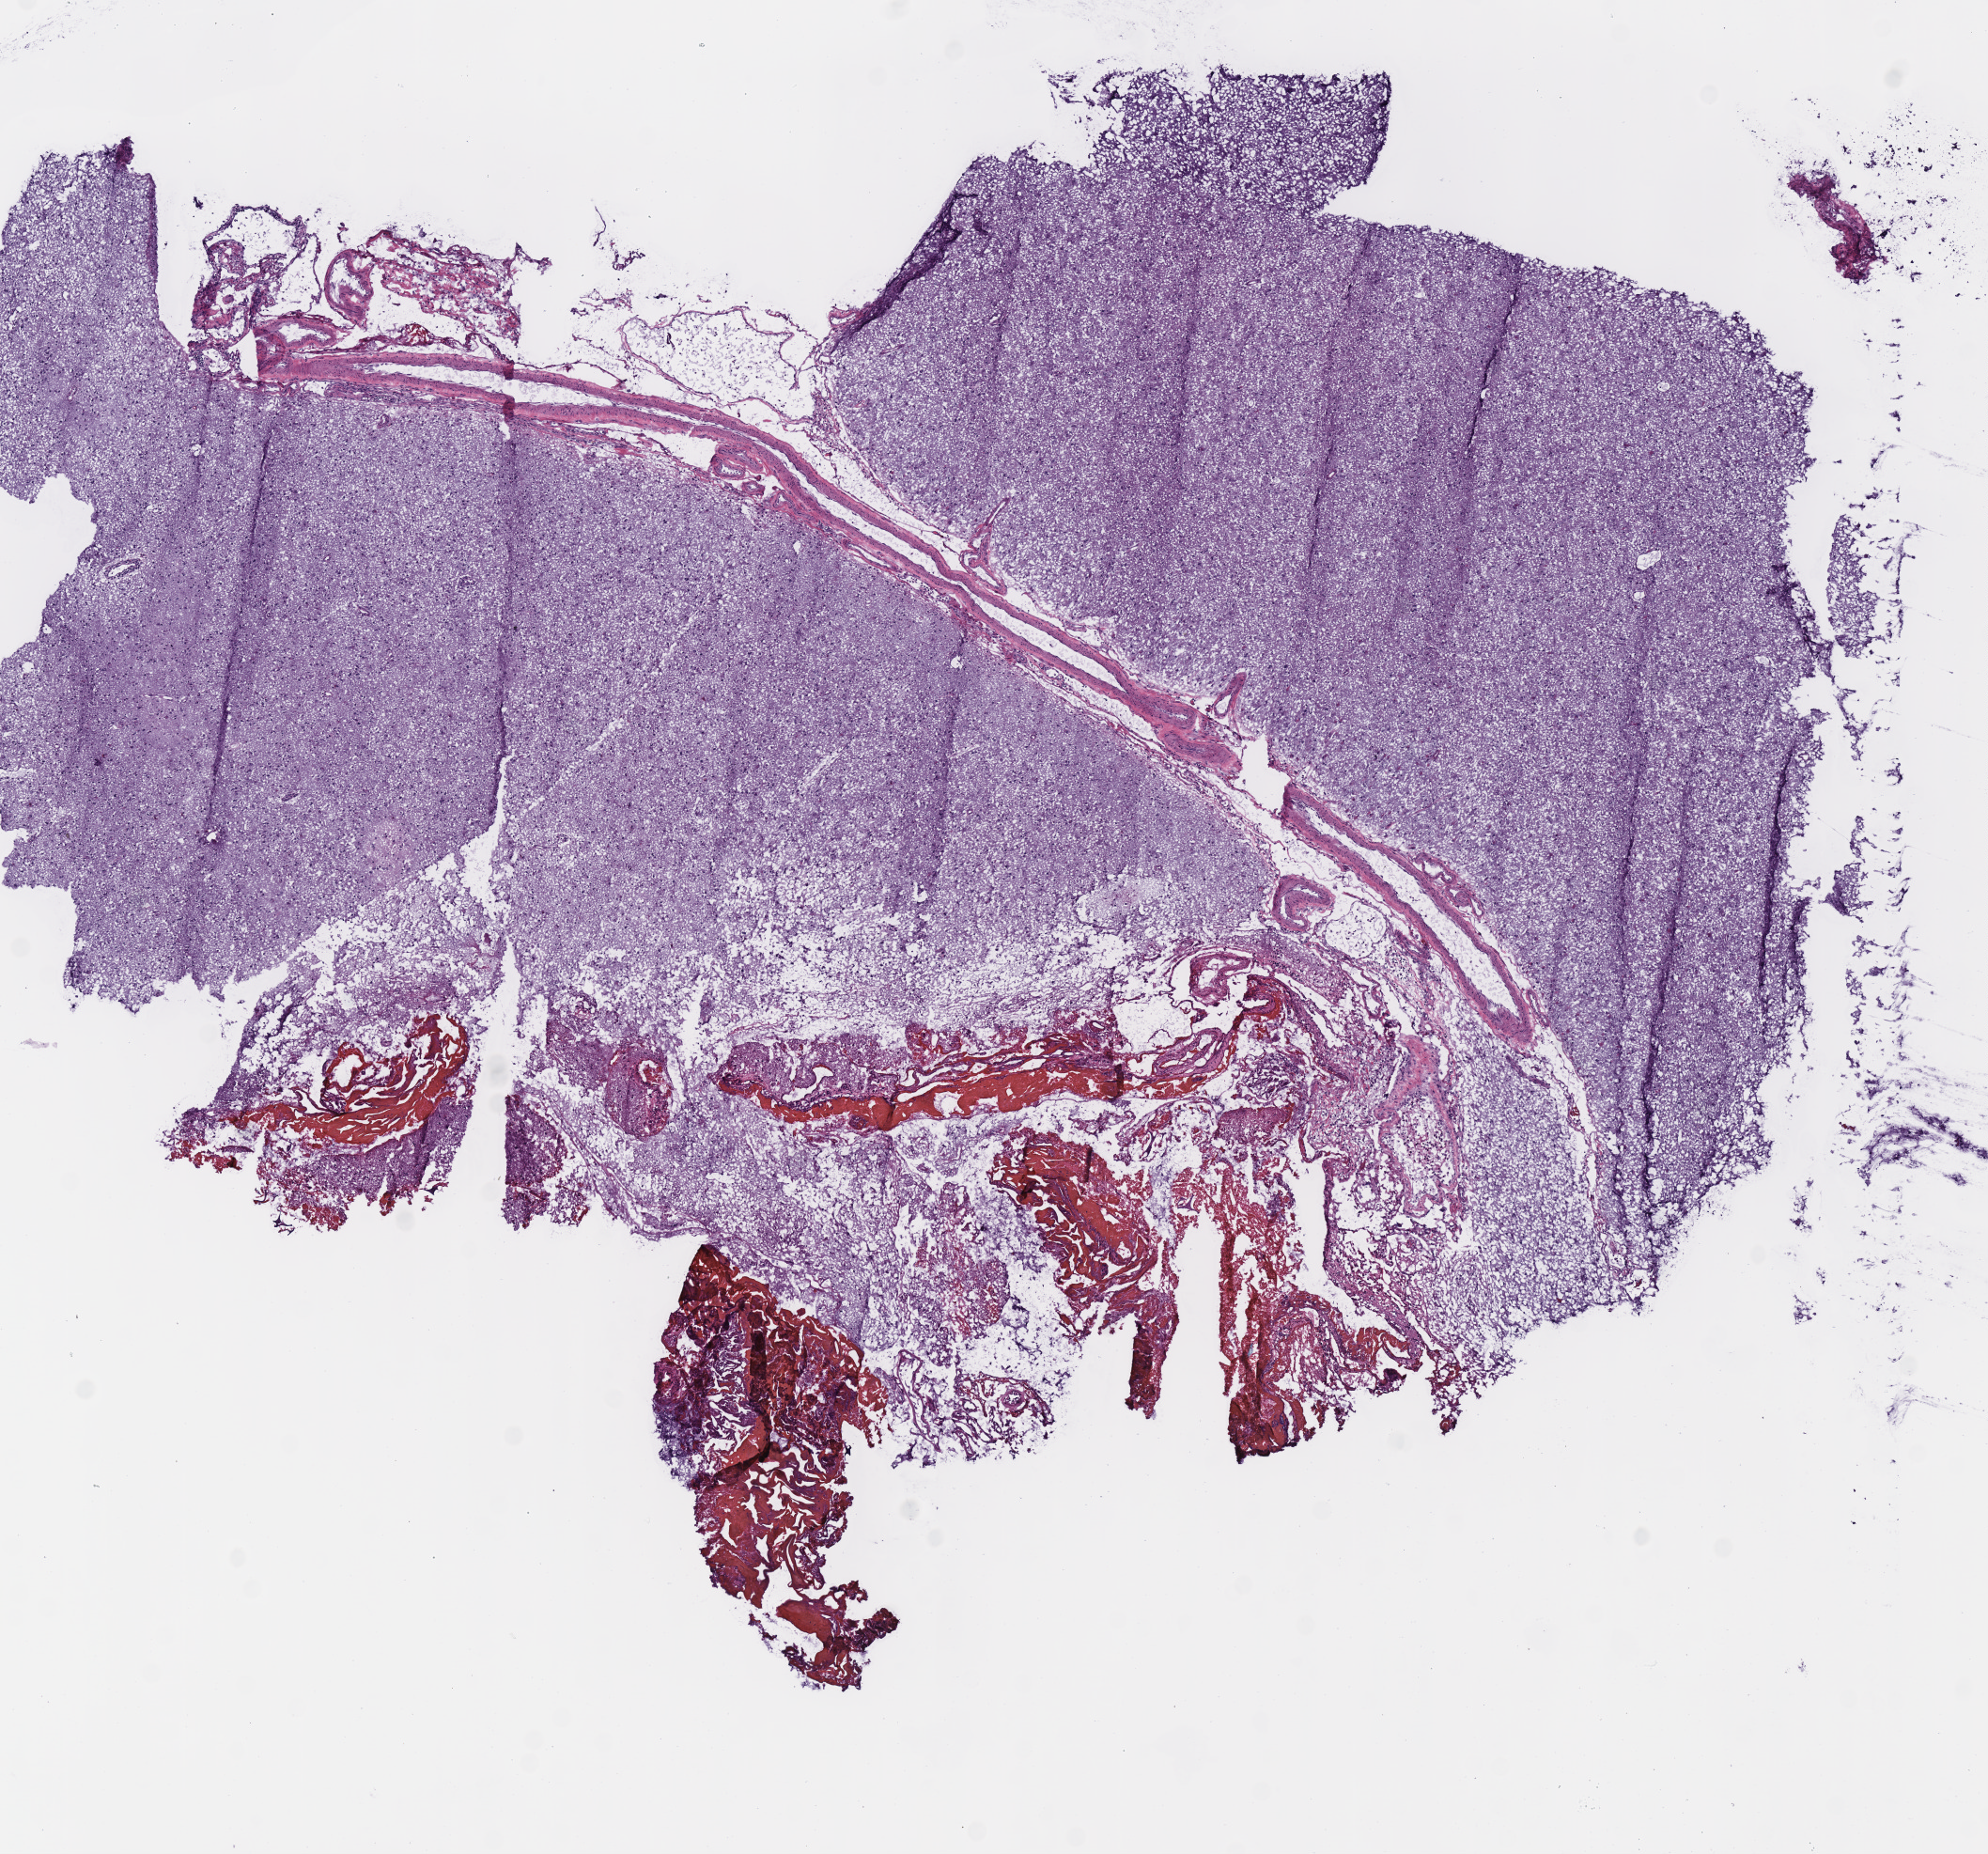
Digitized Hematoxylin and eosin (H&E) stained tissue section (whole slide) — low-resolution overview of the scanned area, about 8.3 x 7.8 mm (slide scanned at 40x); frozen section; sample: primary tumour, brain. Female patient; age at initial diagnosis 40 years. Histologic grade: G2 (moderately differentiated). Pathologist review of this section (percent, as recorded): tumour cells 100%, tumour nuclei 60%, normal cells 0%, stromal cells 0%, necrosis 0%.
* histologic diagnosis: Mixed glioma (cerebrum)